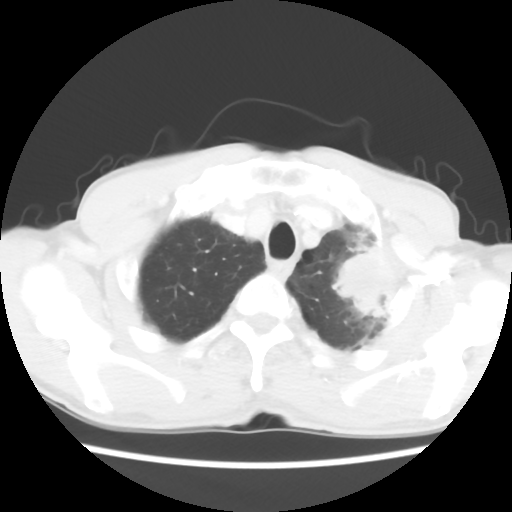
Chest CT, one axial slice. Position 52 of 60 along the scan axis. Reconstruction kernel STANDARD. 120 kVp. Lung window (W 1500 / L -600 HU). 5 mm slice thickness. 512 × 512 image matrix, field of view 308 × 308 mm. Male patient, age 64 years. Case-level facts recorded for this patient, not image findings: clinical TNM (as recorded): T3 N3 M0; histopathological grade: G3.
Outlined on this slice (rectangle marked by the reading radiologist):
- lung tumour (recorded histology: adenocarcinoma): bounding box <325,239,404,334> (left, top, right, bottom; pixels)